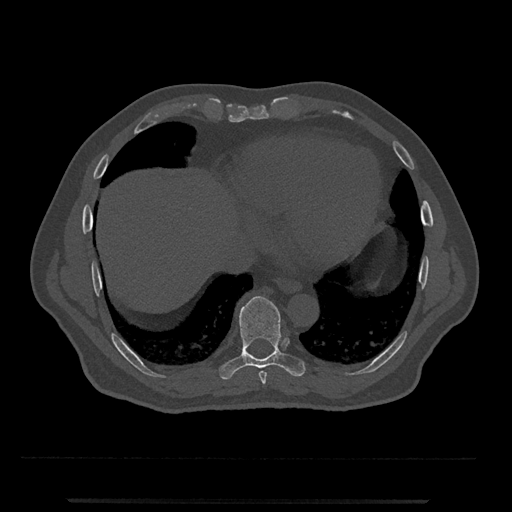
CT including the spine, one axial slice. Position 580 of 797 along the scan axis. Reconstruction kernel Br40s/3. Bone window (W 1800 / L 400 HU). 0.5 mm slice thickness. 512 × 512 image matrix, field of view 419 × 419 mm. Patient: male, 63 years. Case-level facts recorded for this patient, not image findings: primary cancer: prostate.
Annotated regions visible in this slice (semi-automatic segmentation, software-assisted and operator-edited):
- T8 vertebra: bounding box (x1, y1, x2, y2) in pixels: (259, 371, 267, 384)
- T9 vertebra: (219, 296, 306, 380)